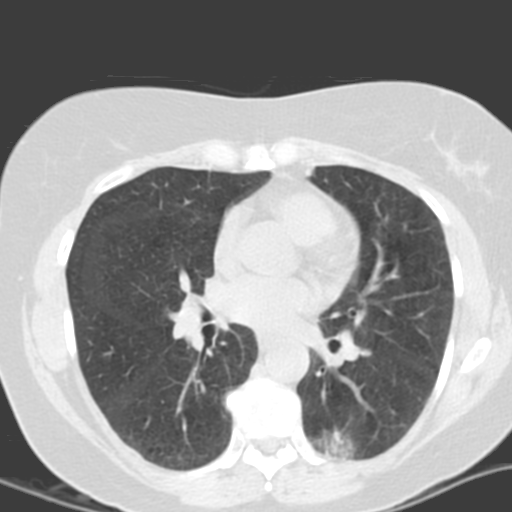
Axial slice from a low-dose chest CT screening exam, second annual screen, lung window (W 1500 / L -600 HU), 3.2 mm slice thickness, standard (soft-tissue) reconstruction kernel (B), slice 72 of 161 in the series. Female participant, aged 55 years at enrolment.
Lesion marked by an expert reader, bounding box [x1, y1, x2, y2] px = [305, 410, 379, 468]. The screening reader recorded 4 non-calcified nodules or masses ≥4 mm on this exam (left lower lobe, left lower lobe, left upper lobe, right middle lobe); which of them this box marks is not recorded. Later outcome: lung cancer diagnosed 688 days after this screen (after the third annual screen) — adenocarcinoma with mixed subtypes, left lower lobe, poorly differentiated (G3), stage IA (AJCC 6th edition), 21 mm at pathology.